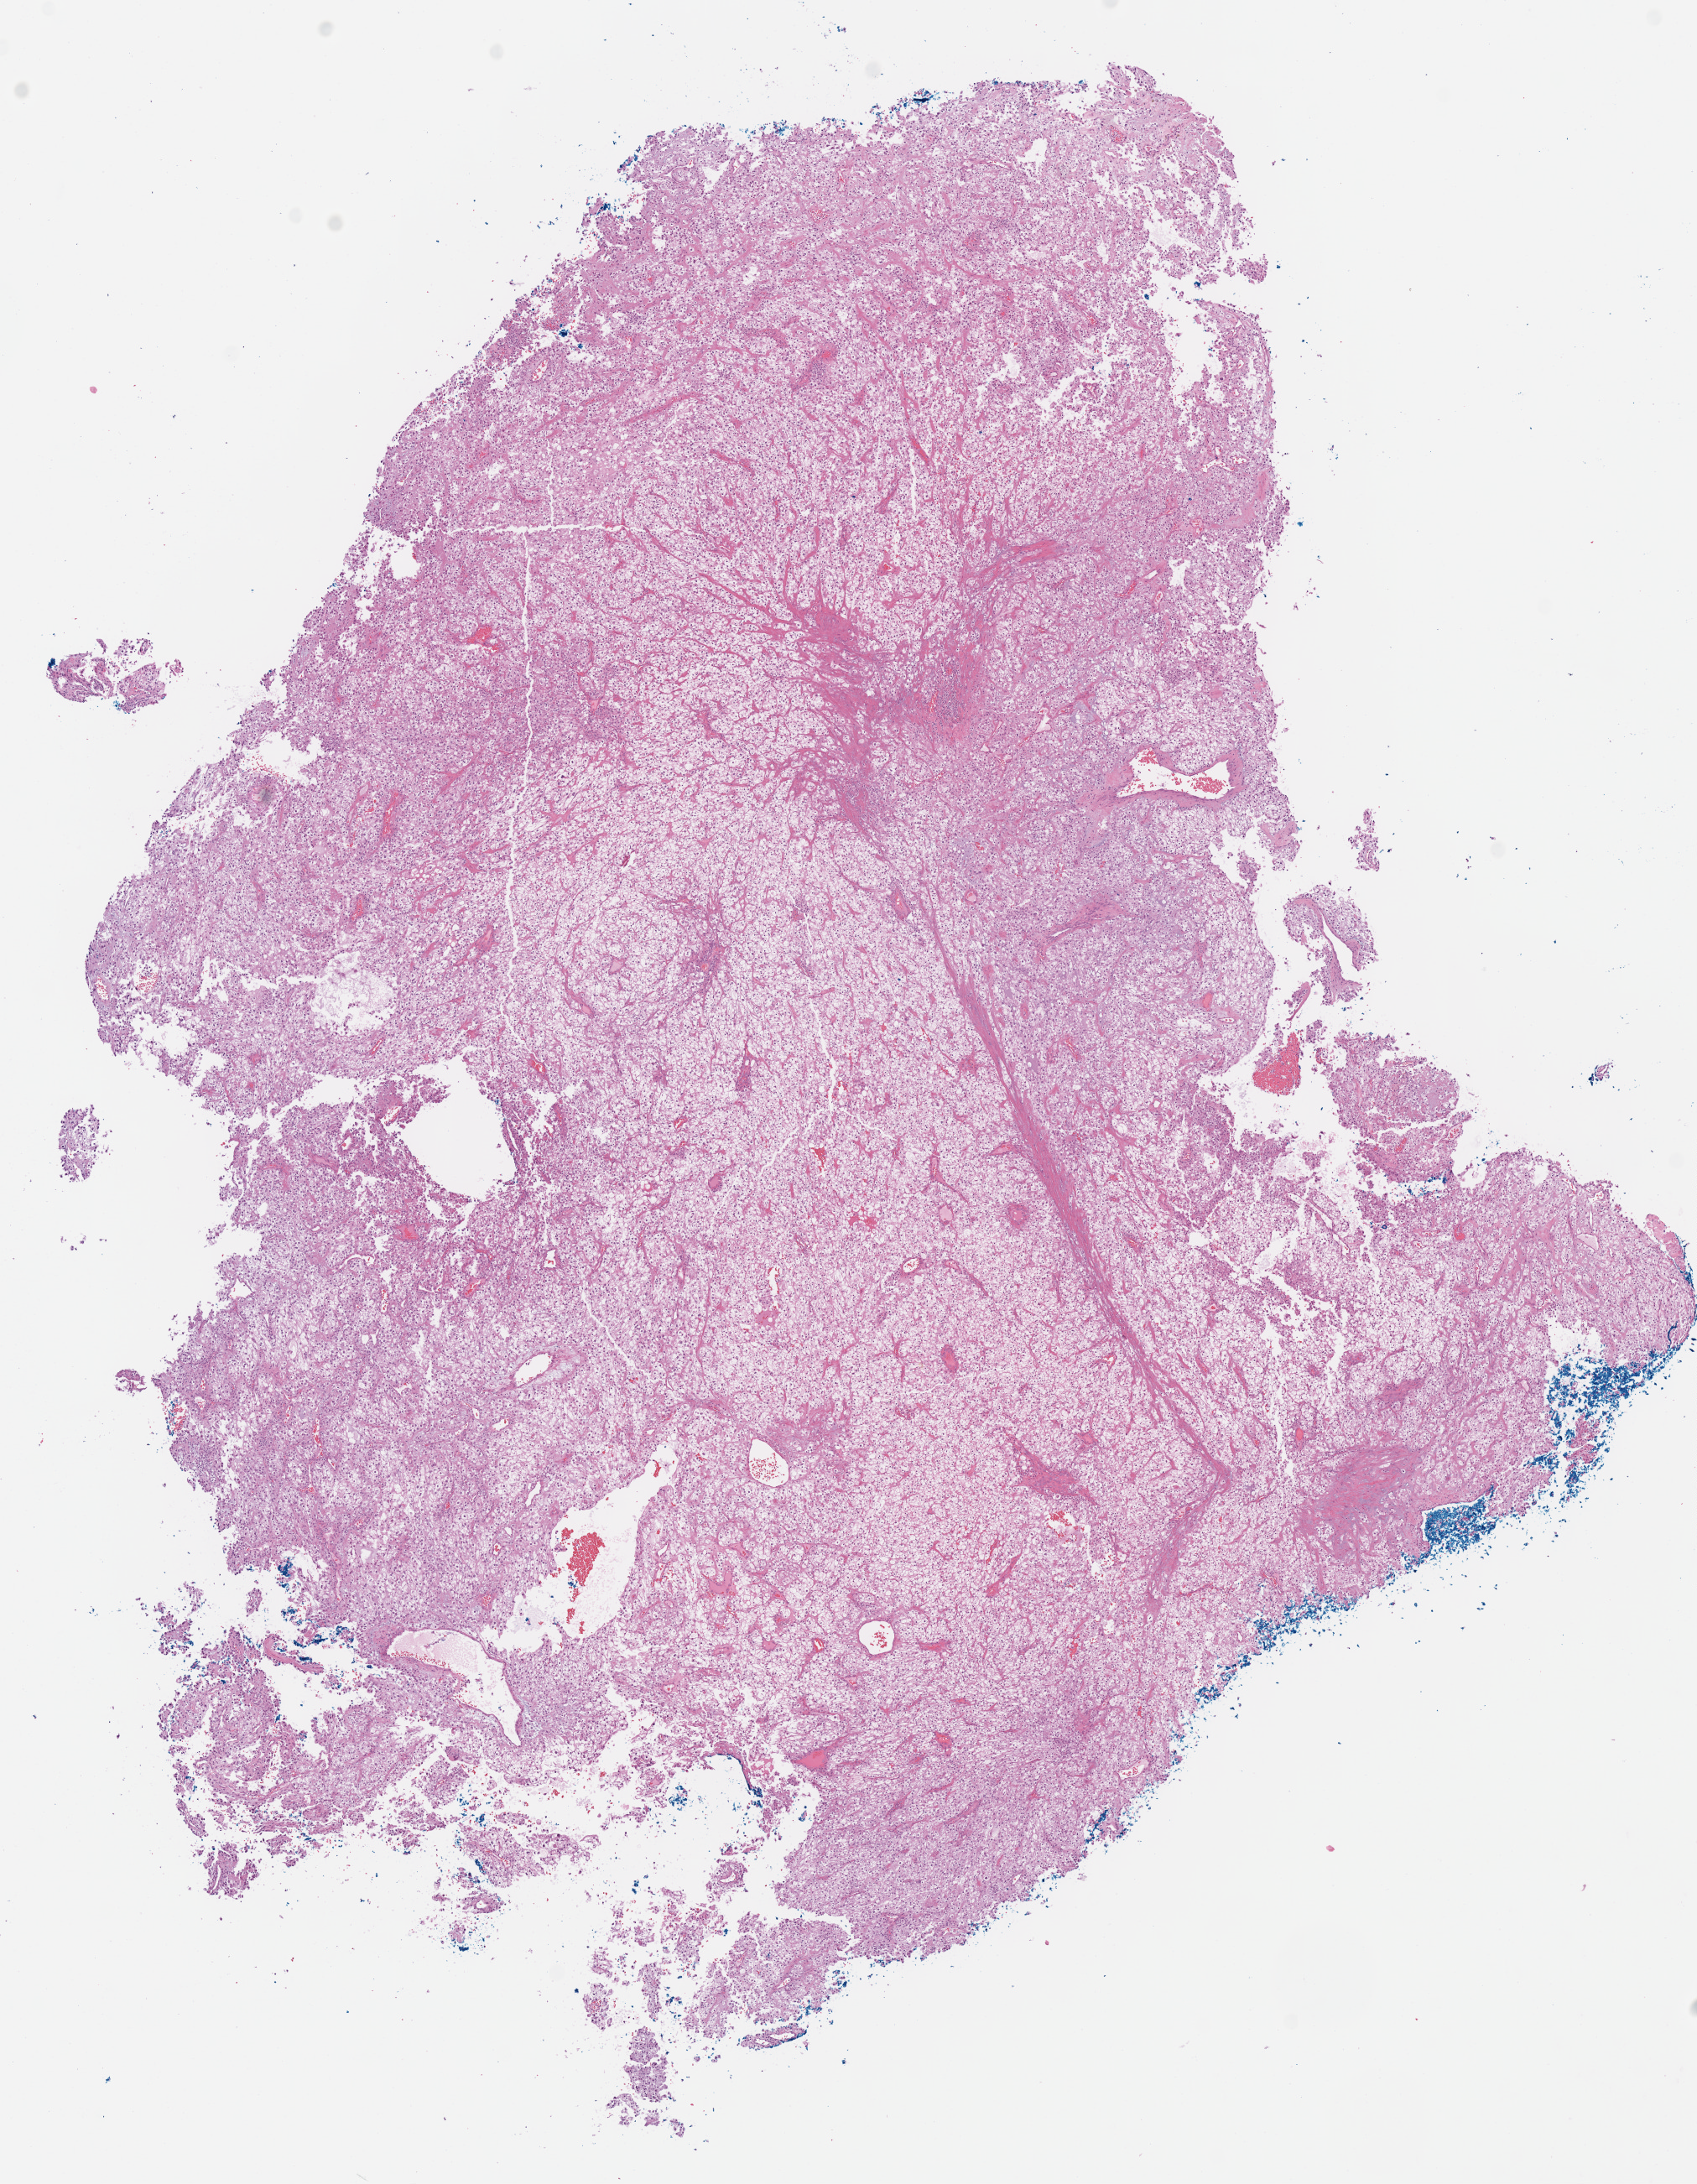
Digitized H&E tissue section (whole slide), whole scanned area (about 8.0 x 10.3 mm, from a 40x scan) shown as a low-resolution overview; formalin-fixed paraffin-embedded (FFPE) diagnostic section; sample: primary tumour, kidney. Female, age 75 years at initial diagnosis. Histologic grade: G4 (undifferentiated).
* laterality: right
* AJCC pathologic stage: I
* TNM: T1 NX M0
* pathologic diagnosis: Clear cell adenocarcinoma, NOS